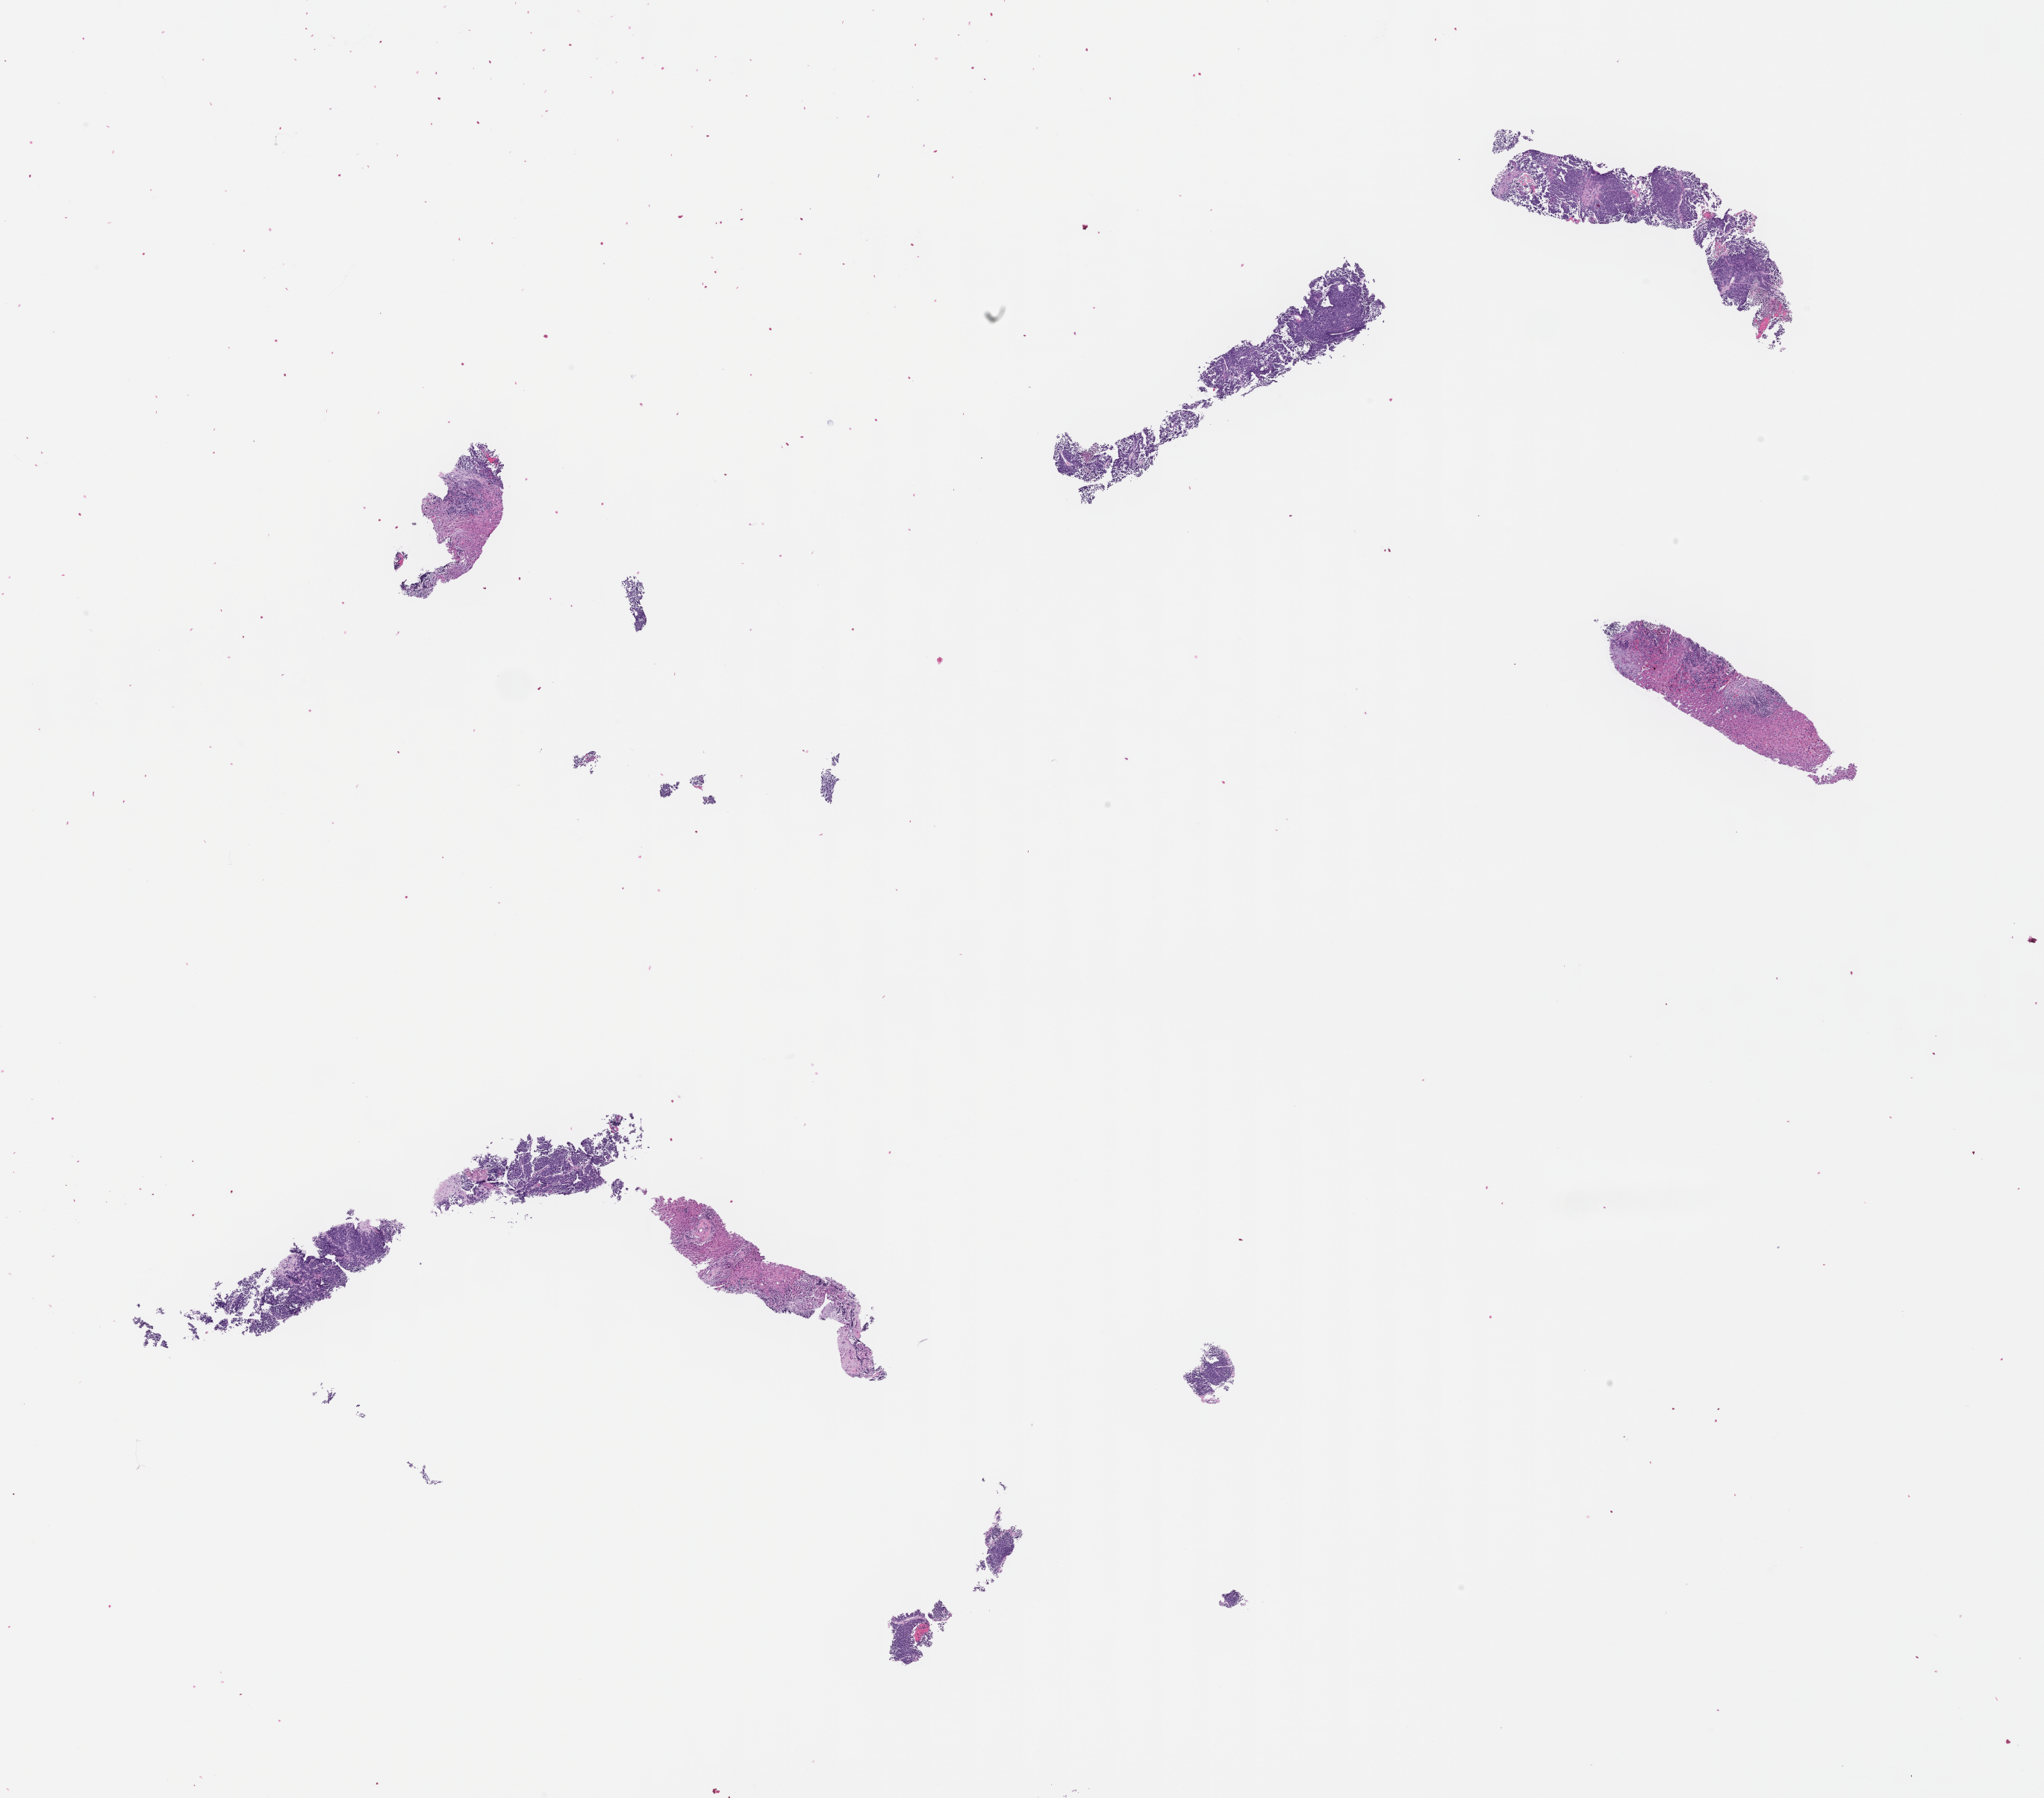
Whole-slide image, haematoxylin and eosin stain, low-resolution overview of the scanned area, about 22.1 x 19.4 mm; formalin-fixed paraffin-embedded section; collected at baseline (before treatment). Patient: male.
This section: metastasis (sampled organ not recorded). Primary diagnosis of the patient: Small Cell Lung Carcinoma.